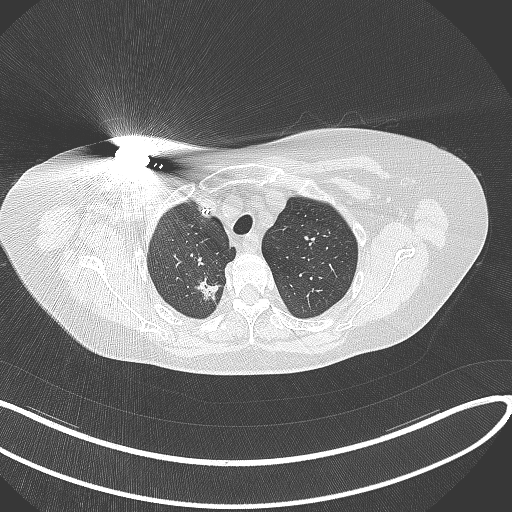
Chest CT, one axial slice; position 276 of 316 along the scan axis; 120 kVp; lung window (W 1500 / L -600 HU); 1 mm slice thickness; 512 × 512 image matrix. Female patient, age 72 years. From the clinical record (not read from this slice): clinical TNM (as recorded): T1c N0 M0.
Annotated regions visible in this slice (rectangle marked by the reading radiologist):
- lung tumour (recorded histology: adenocarcinoma): bounding box <190,273,221,303> (left, top, right, bottom; pixels)